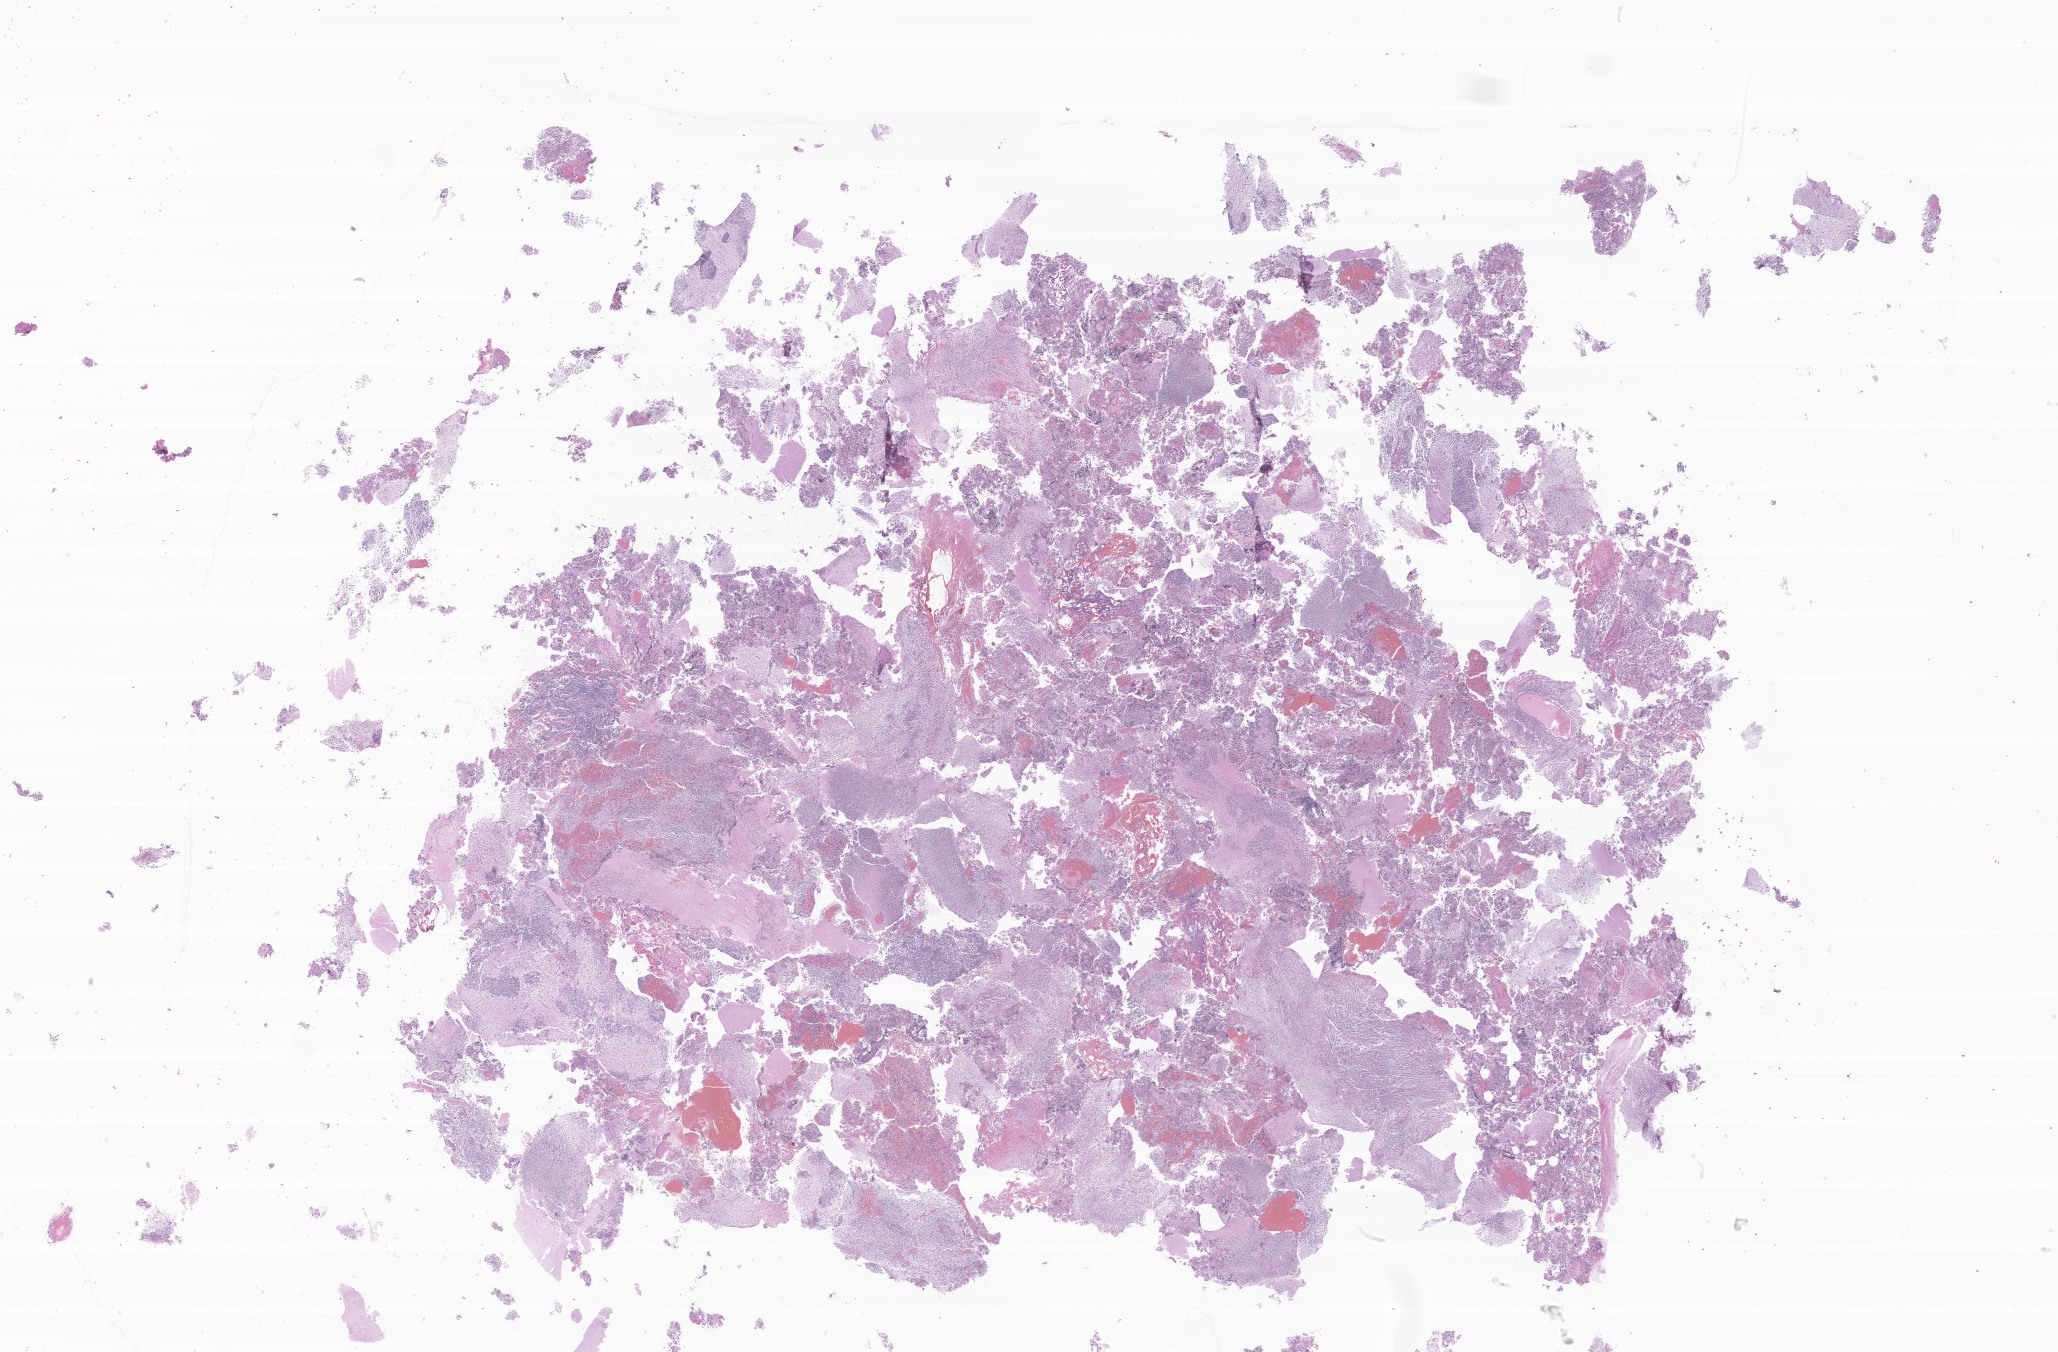
H&E whole-slide image of tumor tissue from the cerebellum — whole scanned area (about 34.7 x 22.8 mm) shown as a low-resolution overview. FFPE section. Patient: male, age 49 months.
Diagnosis (ICD-O-3 morphology term): Medulloblastoma, NOS.